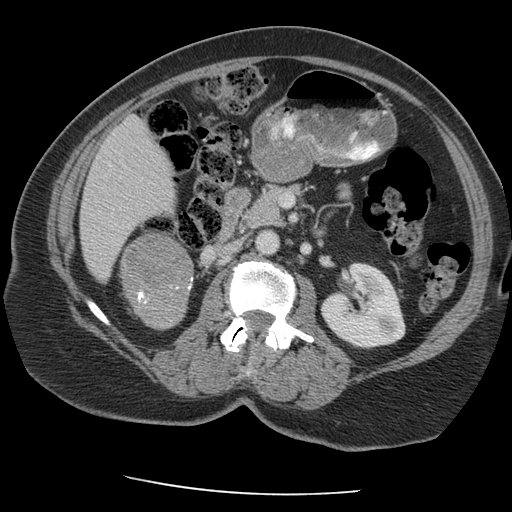
Contrast-enhanced abdominal CT, one axial slice; position 109 of 163 along the scan axis; intravenous contrast given; soft-tissue window (W 400 / L 40 HU); 512 × 512 image matrix, field of view 360 × 360 mm. Female patient, age 70 years. From the clinical record (not read from this slice): diagnosis: adrenocortical carcinoma; tumour side: right adrenal; tumour size at pathology: 9.5 cm; Ki-67 index: 5 %; stage (as recorded): 2.
Structures marked on this image (semi-automatically segmented with operator editing):
- mass: bounding box [x1, y1, x2, y2] px = [123, 235, 193, 328]